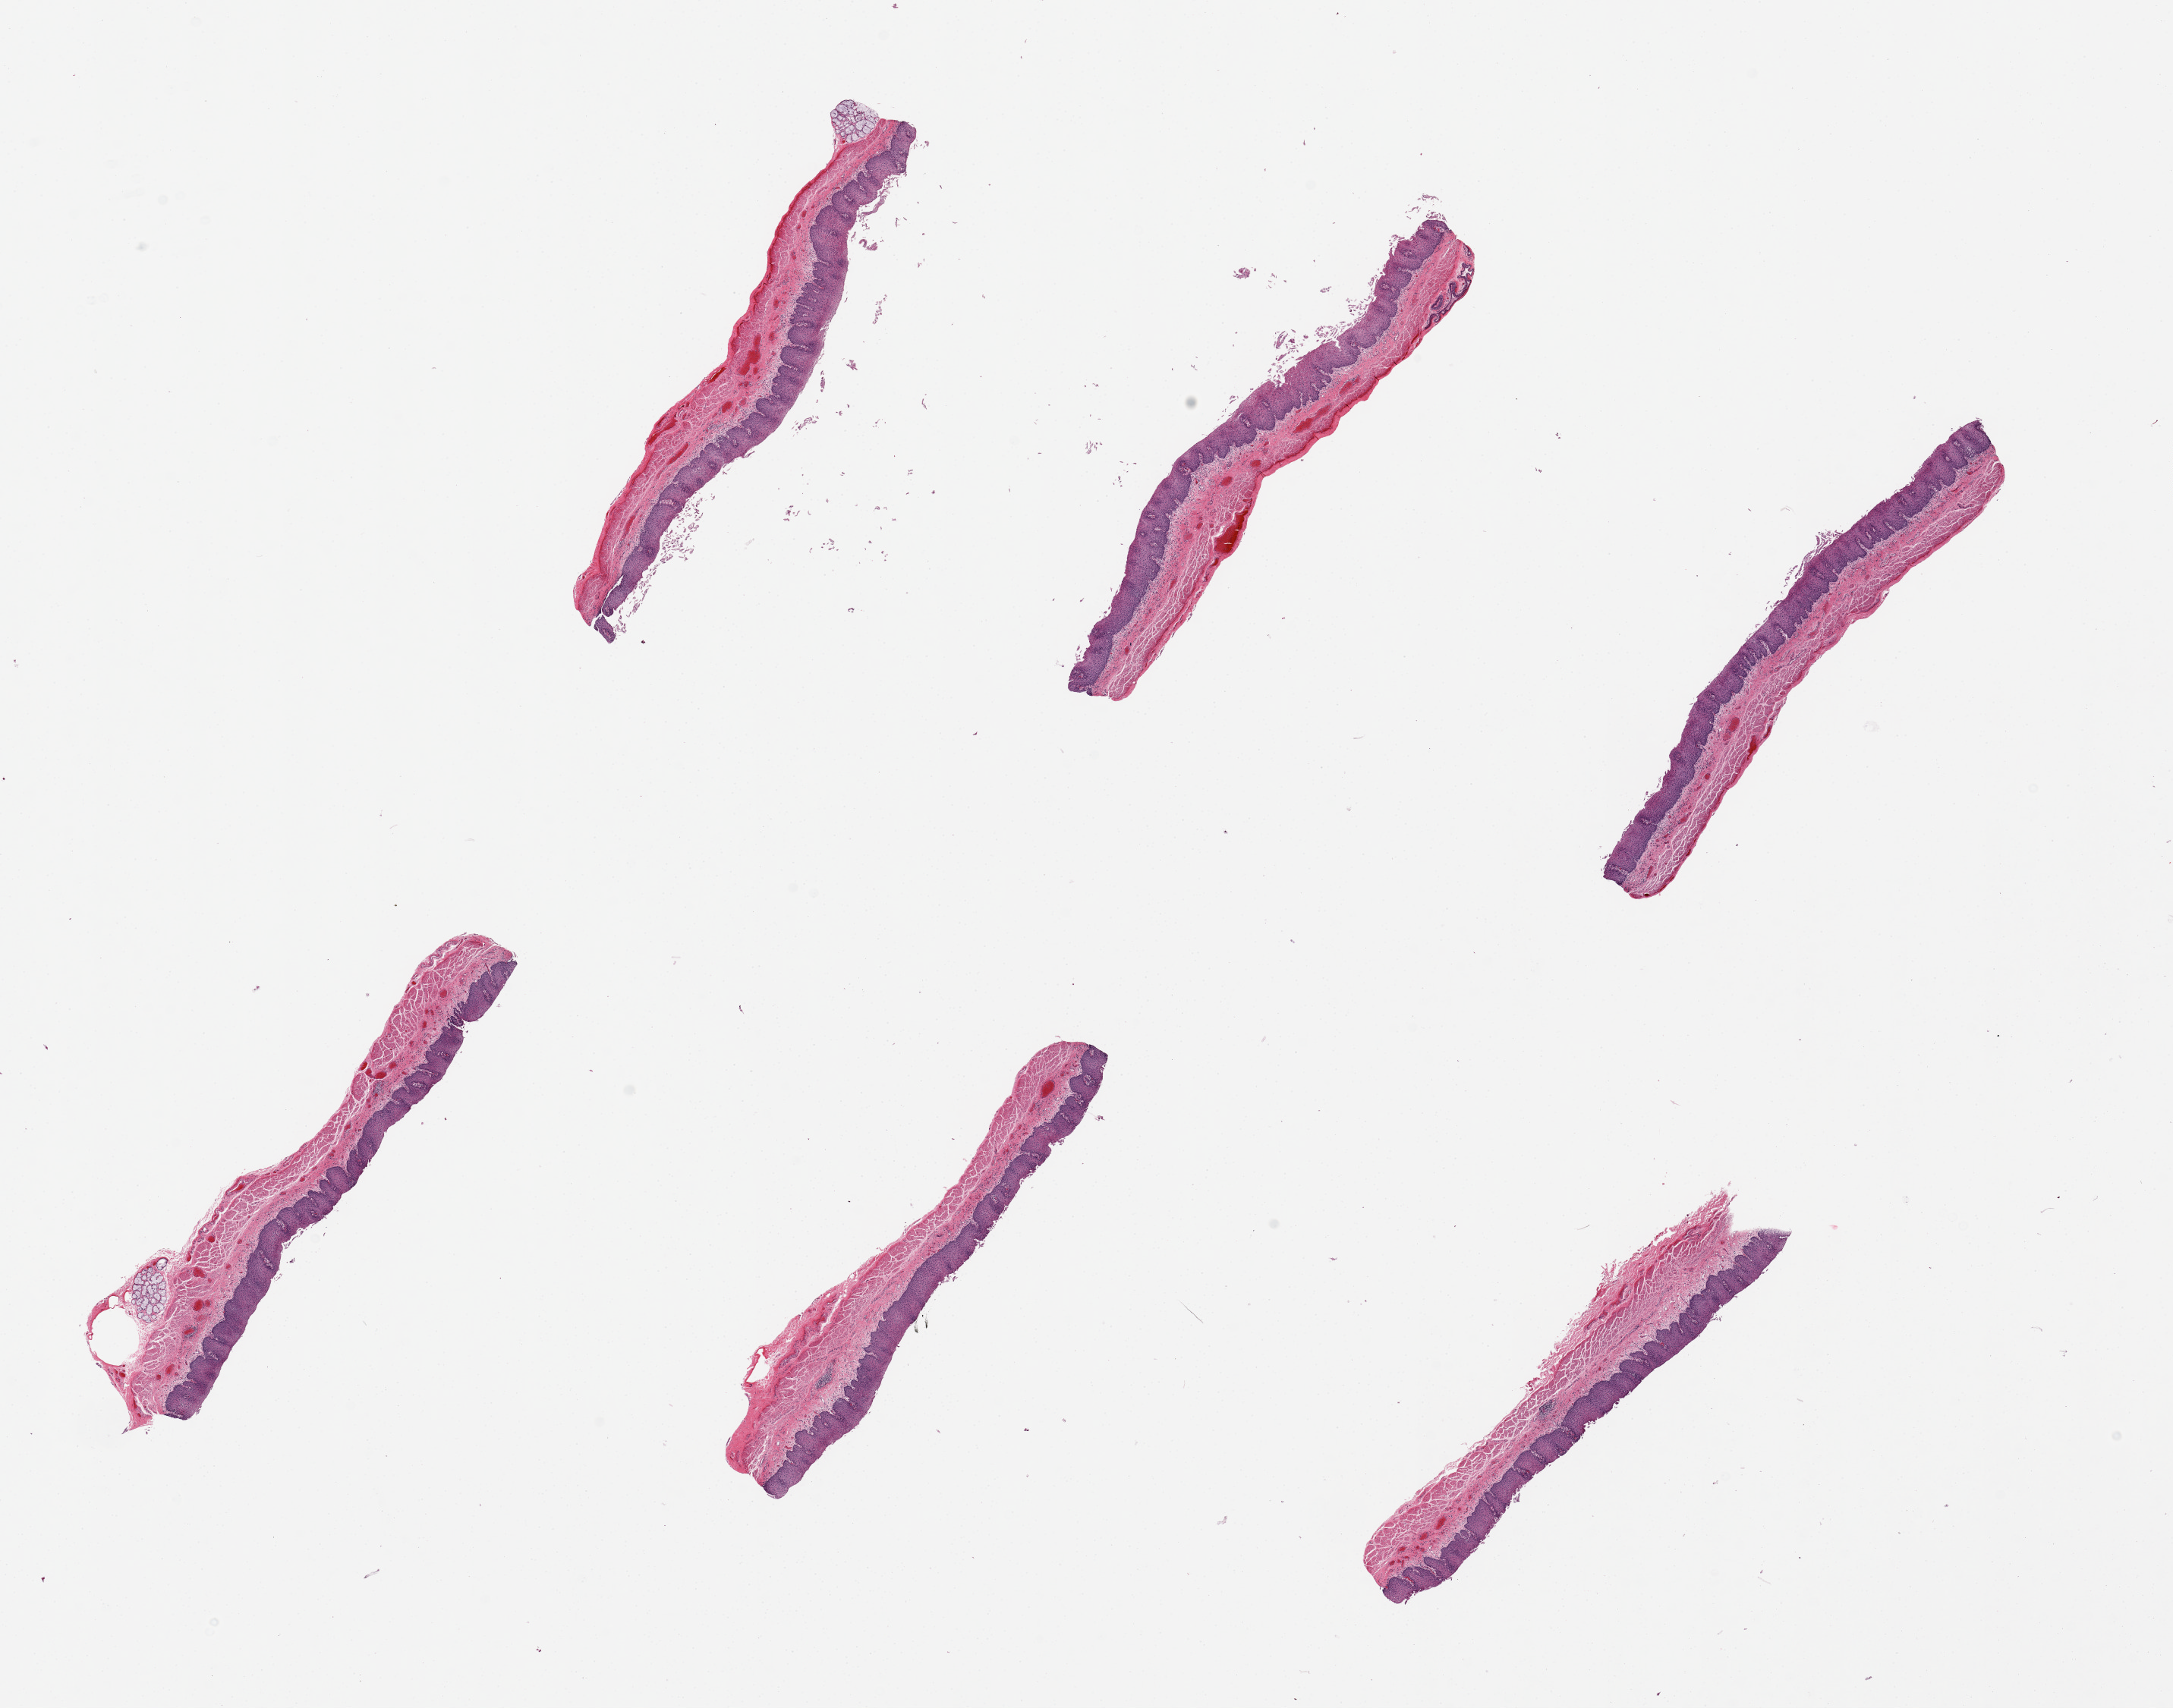
Whole-slide image, haematoxylin and eosin stain, brightfield, whole scanned area (about 22.6 x 17.8 mm) shown as a low-resolution overview, PAXgene-fixed paraffin-embedded (PFPE) section, sampled site (target tissue): esophageal mucous membrane, donor tissue sample.
* reviewer comment on this tissue sample: 6 pieces. well trimmed